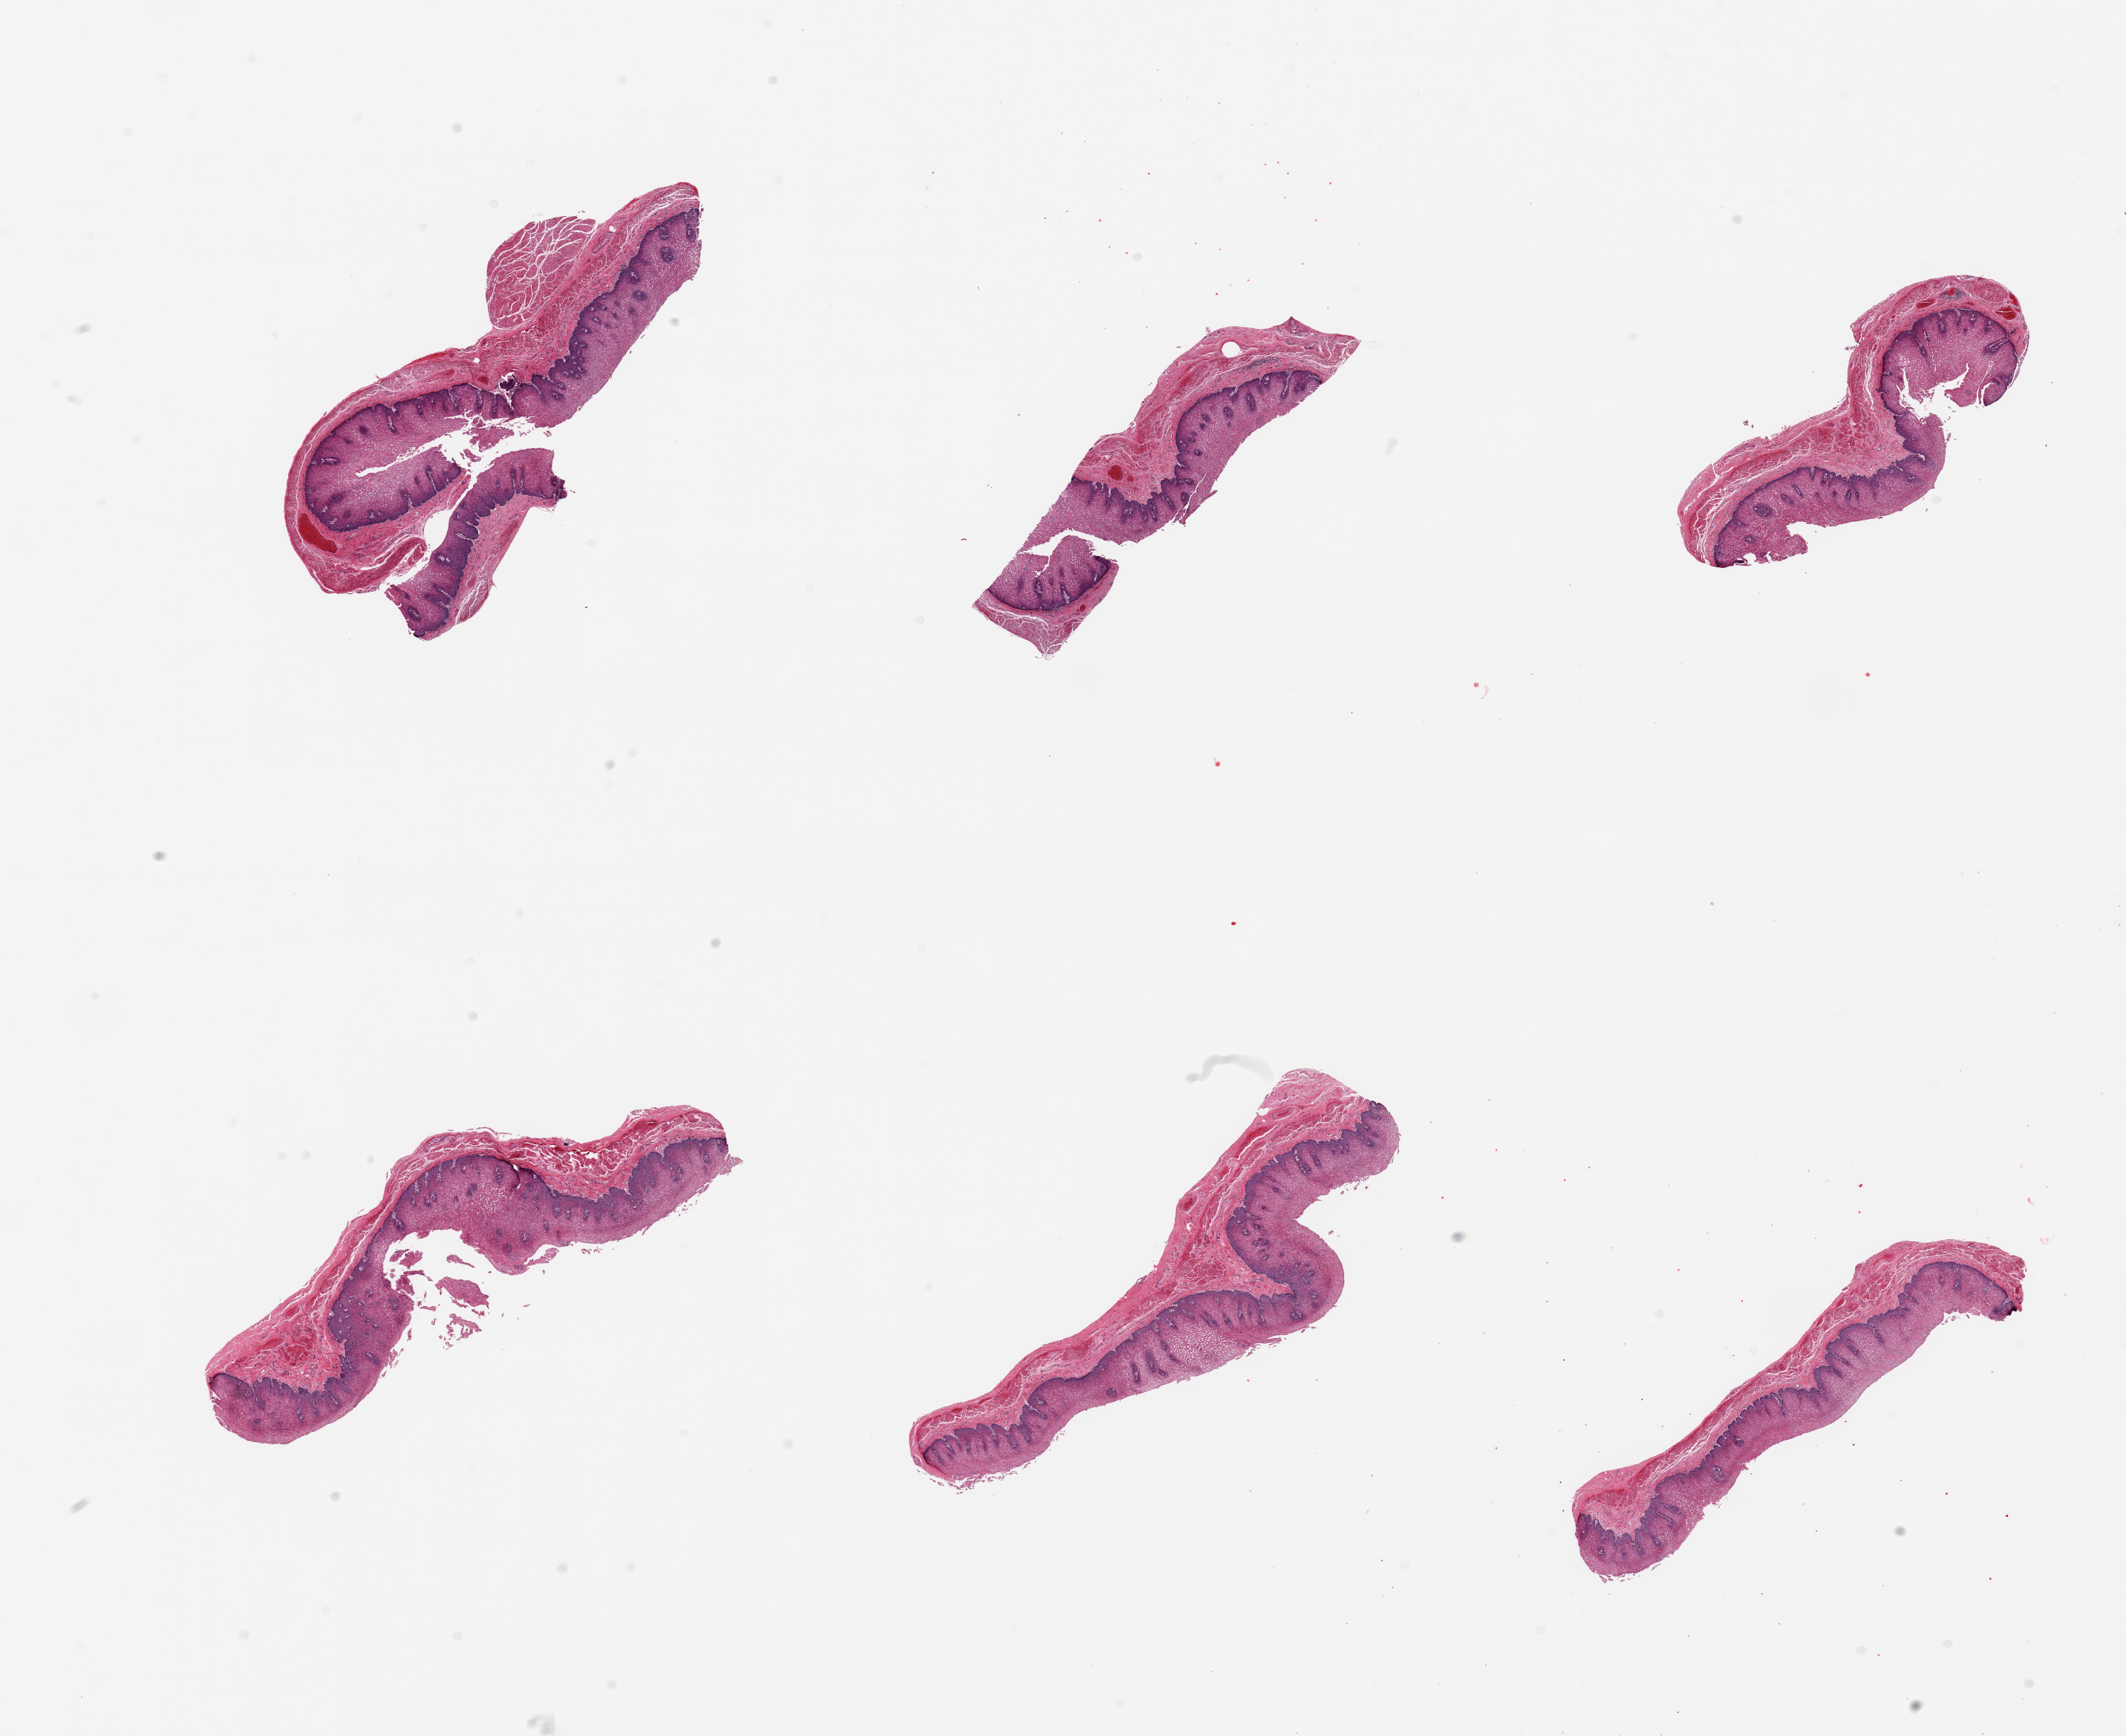
Whole-slide image, hematoxylin and eosin (H&E) stain, a low-resolution overview of the entire scanned area, about 22.6 x 18.5 mm (from a 20x scan). PAXgene-fixed, paraffin-embedded tissue. Sampled site (target tissue): esophageal mucous membrane. Tissue donor sample.
* pathologist's review note for this sample: 6 pieces, squamous mucosa up to ~0.5mm, ~50% thickness